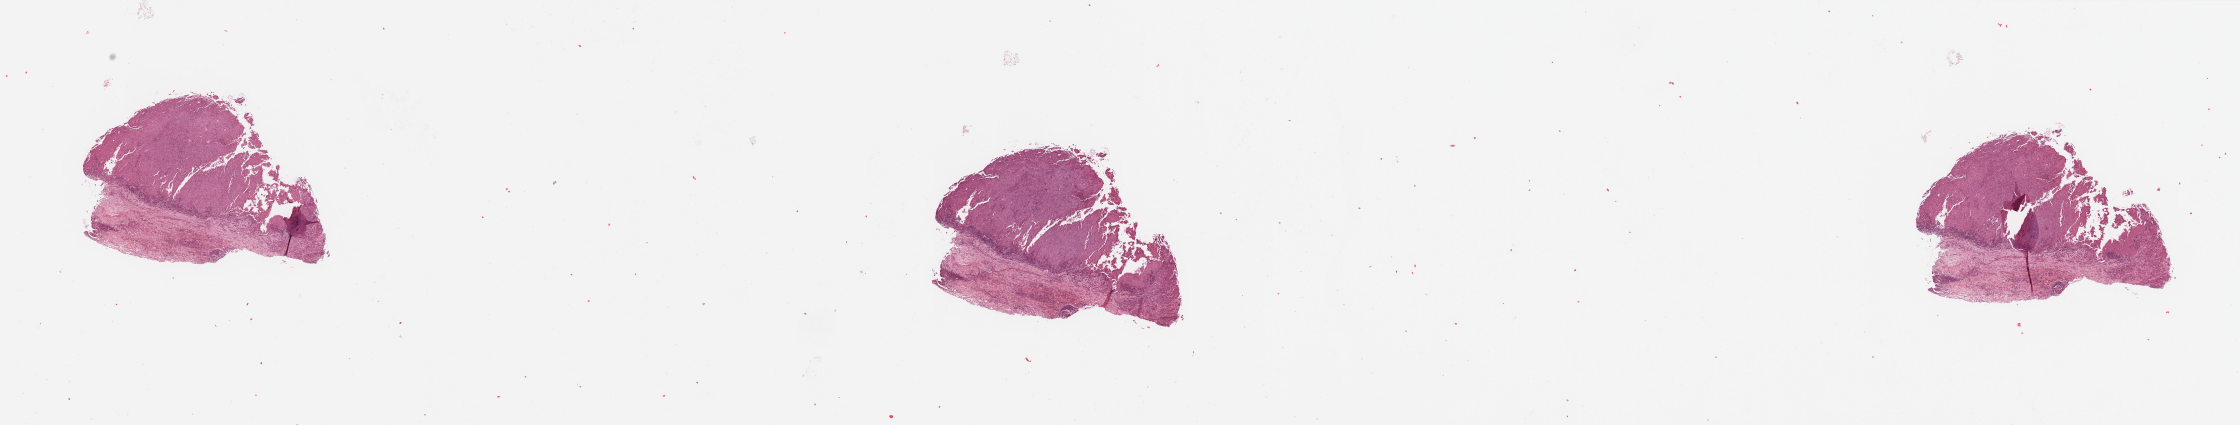
Whole-slide histology image, H&E, shown as a low-resolution overview of the whole scanned area (about 35.4 x 6.7 mm, from a 20x scan), lung, tumour tissue. 60-year-old female patient. Histologic grade: G3 (poorly differentiated).
AJCC pathologic stage: IIB. Diagnosis: Adenocarcinoma, NOS. Primary tumour site (as recorded): right lower lobe.